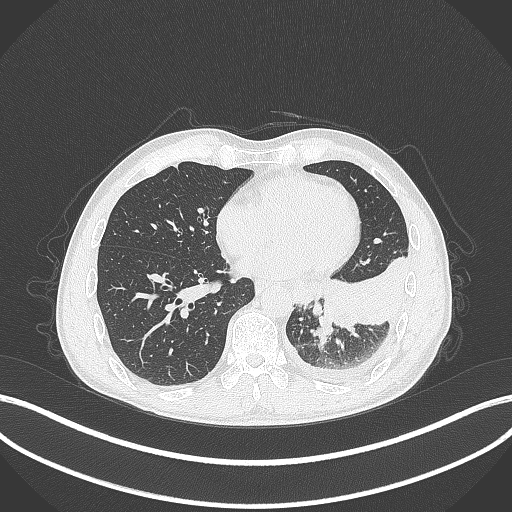
Chest CT, one axial slice; slice 106 of 295 in the series (ordered by position); reconstruction kernel B70f; lung window (W 1500 / L -600 HU); 512 × 512 image matrix, field of view 400 × 400 mm. Patient: male, 47 years. Case-level facts recorded for this patient, not image findings: clinical TNM (as recorded): T3 N1 M1c; histopathological grade: G3.
Annotated regions visible in this slice (bounding box drawn by a radiologist):
- lung tumour (recorded histology: small cell carcinoma): bounding box (x1, y1, x2, y2) in pixels: (310, 315, 331, 346)